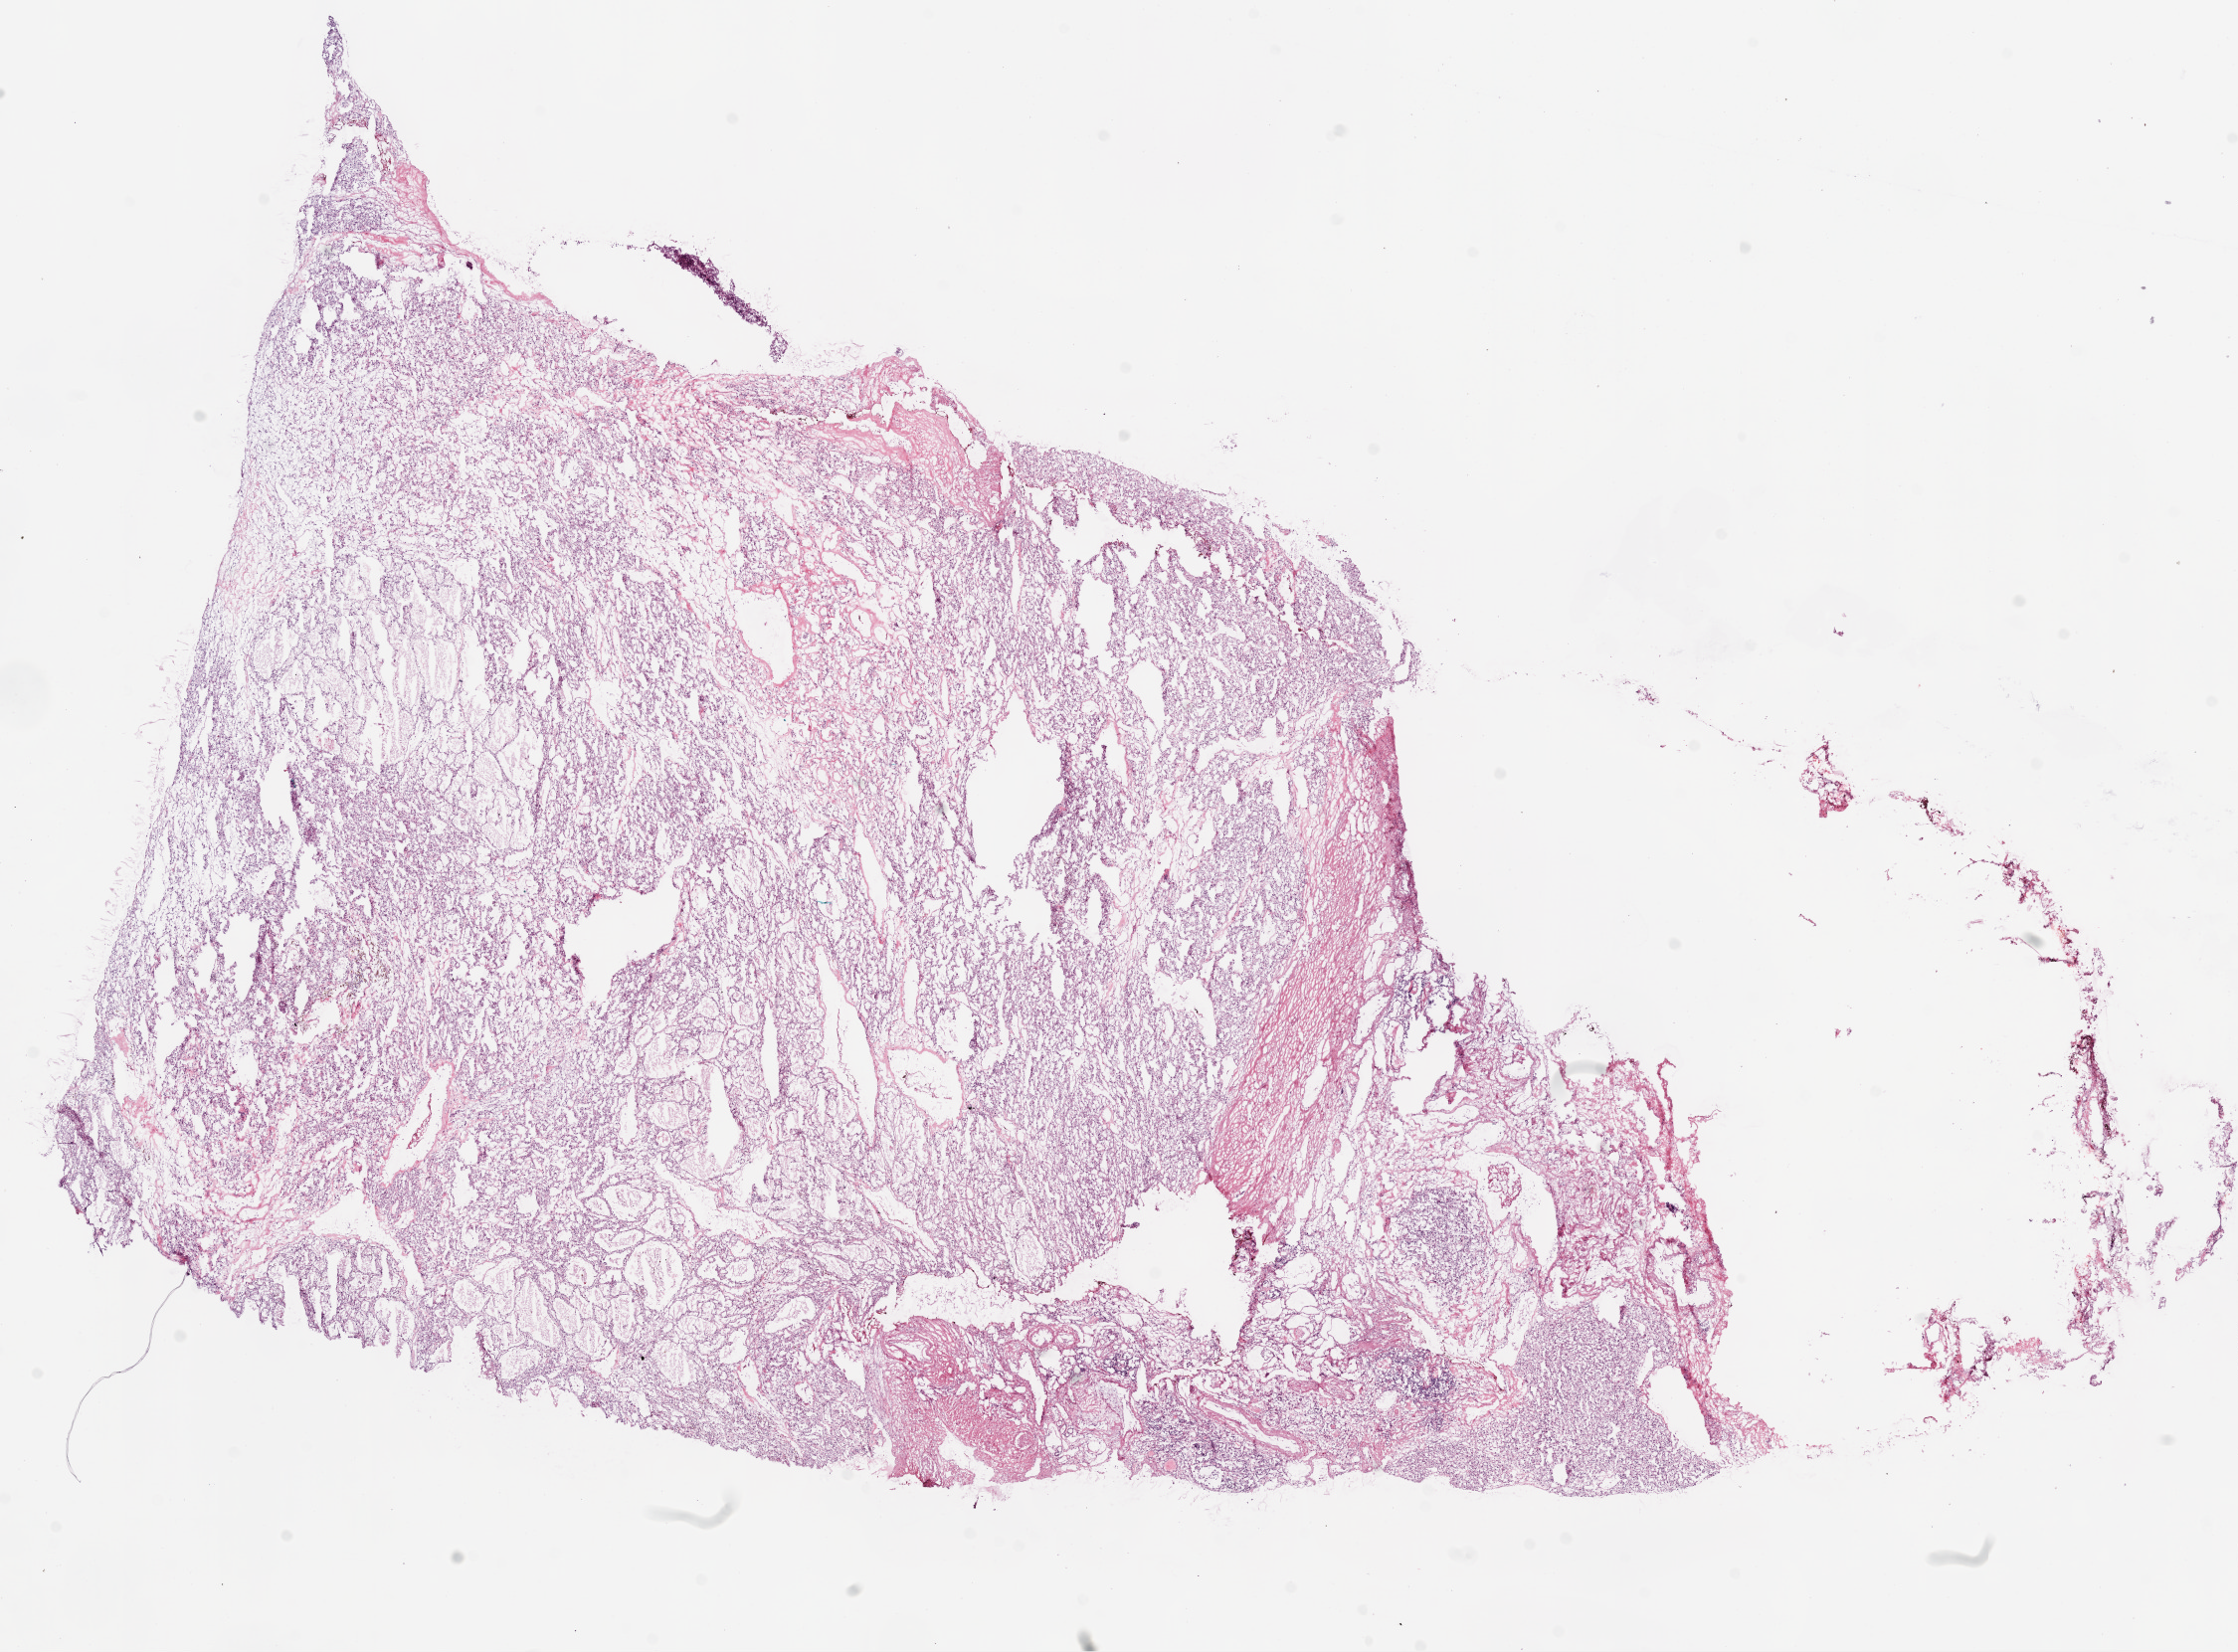
Digitized Hematoxylin and eosin (H&E) stained tissue section (whole slide) — shown as a low-resolution overview of the whole scanned area (about 18.1 x 13.3 mm). Frozen section from the top of the tissue portion. Sample: primary tumour, kidney. Female, age 75 years at initial diagnosis. Histologic grade: G2 (moderately differentiated). Composition of this section per pathologist review: tumour cells 90%, tumour nuclei 80%, normal cells 0%, stromal cells 10%, necrosis 0%.
• AJCC pathologic stage: I
• TNM: T1a N0 M0
• laterality: right
• pathologic diagnosis: Clear cell adenocarcinoma, NOS